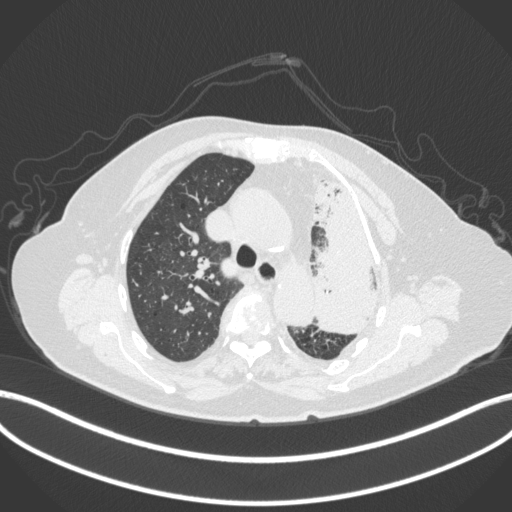
Chest CT, one axial slice; slice 284 of 399 in the series (ordered by position); 120 kVp; lung window (W 1500 / L -600 HU); 512 × 512 image matrix. Female patient, age 75 years. Case-level facts recorded for this patient, not image findings: clinical TNM (as recorded): T3 N3 M1.
Outlined on this slice (rectangle marked by the reading radiologist):
- lung tumour (recorded histology: adenocarcinoma): box from (x=310, y=178) to (x=396, y=336) px